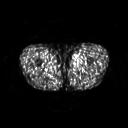
FDG PET of an extremity soft-tissue mass (from a PET/CT study), one axial slice. Position 256 of 311 along the scan axis. 128 × 128 image matrix, field of view 500 × 500 mm. Patient: male, 29 years. Case-level facts recorded for this patient, not image findings: histological type: mixoid liposarcoma; grade: low; site of the primary tumour: left thigh.
Structures marked on this image (expert contour drawn on MRI and transferred to this co-registered scan by the dataset authors):
- gross tumour volume (mass): box from (x=72, y=55) to (x=82, y=65) px